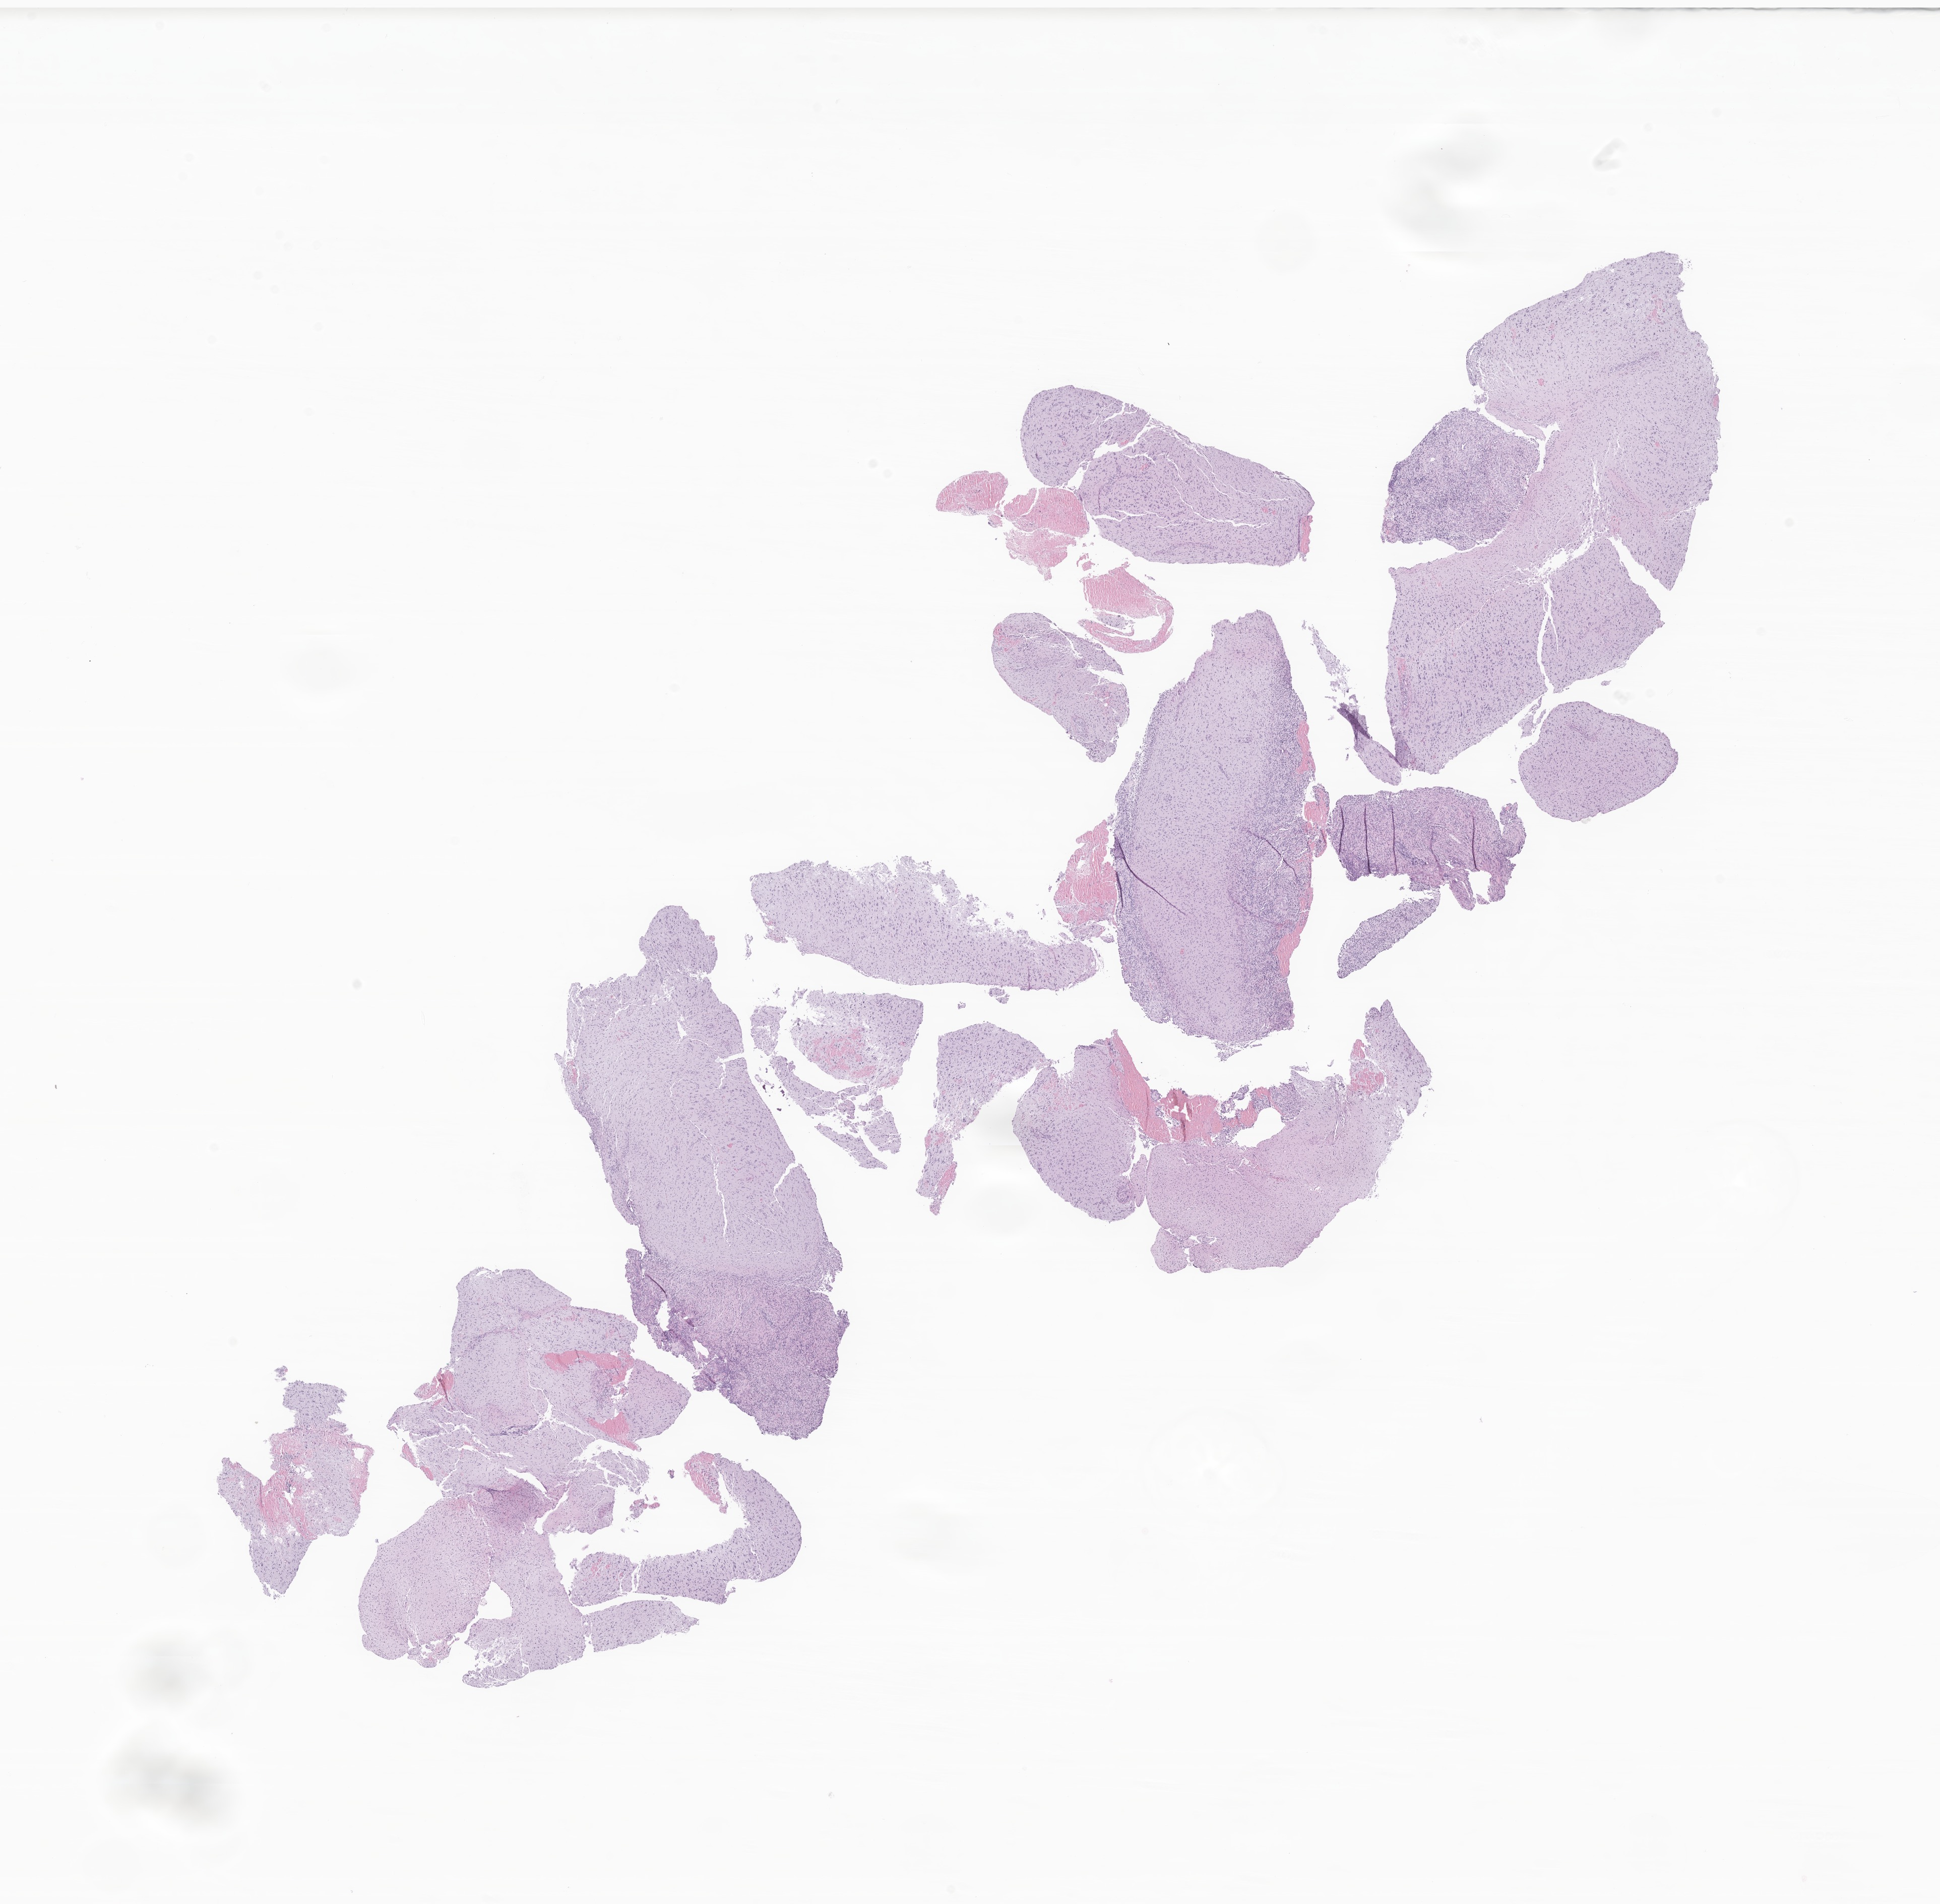
Haematoxylin and eosin whole-slide image of tumor tissue from the parietal lobe, shown as a low-resolution overview of the whole scanned area (about 16.2 x 15.9 mm). FFPE section. Patient male; age 209 months (17 years 5 months).
Recorded diagnosis: Glioma, malignant.